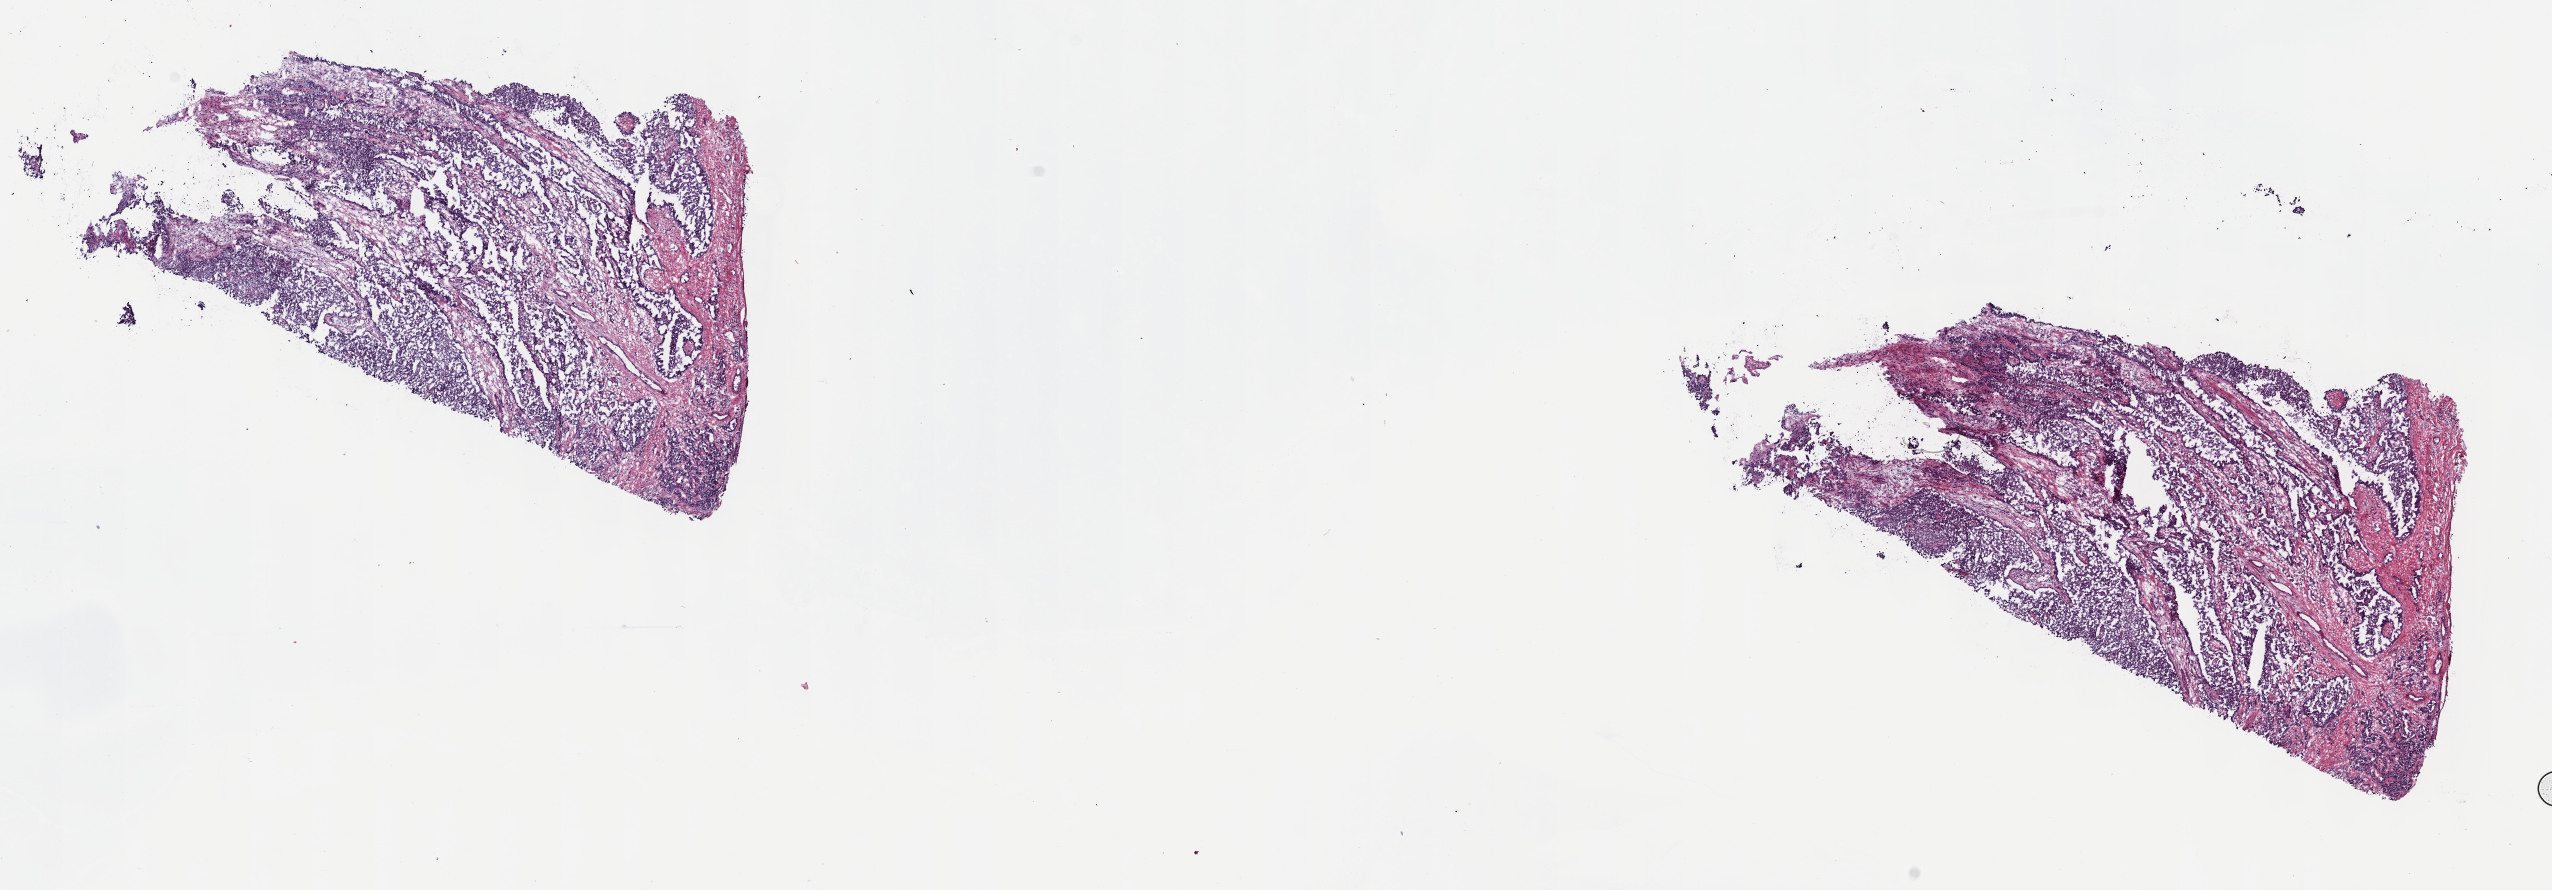
Digitized Hematoxylin and eosin (H&E) stained tissue section (whole slide) — shown as a low-resolution overview of the whole scanned area (about 20.6 x 7.2 mm). Frozen section from the top of the tissue portion. Sample: primary tumour, mesothelium. Patient: male, age at initial diagnosis 60 years. Composition of this section per pathologist review: tumour cells 75%, tumour nuclei 75%, normal cells 0%, stromal cells 25%, necrosis 0%. Infiltration values recorded for this section: lymphocyte infiltration 3%, monocyte infiltration 1%, neutrophil infiltration 5%.
AJCC pathologic stage: IV (7th edition). Diagnosis: Epithelioid mesothelioma, malignant. Laterality: right.